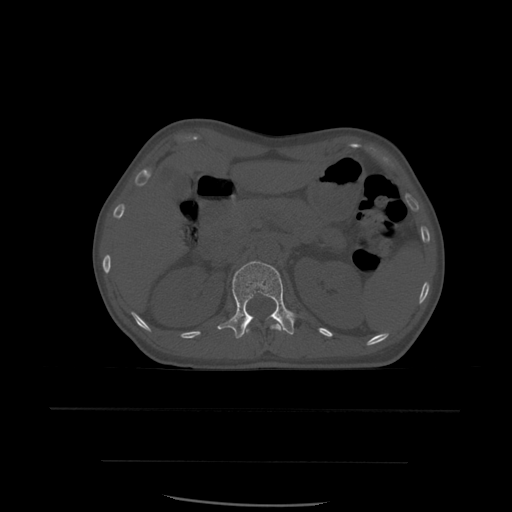
CT including the spine, one axial slice; slice 254 of 574 in the series (ordered by position); bone window (W 1800 / L 400 HU); 512 × 512 image matrix, field of view 392 × 392 mm. Patient age 48 years. Case-level facts recorded for this patient, not image findings: primary cancer: lung.
Structures marked on this image (semi-automatic segmentation, software-assisted and operator-edited):
- L1 vertebra: bounding box (x1, y1, x2, y2) in pixels: (218, 261, 295, 339)
- T12 vertebra: (246, 319, 283, 334)